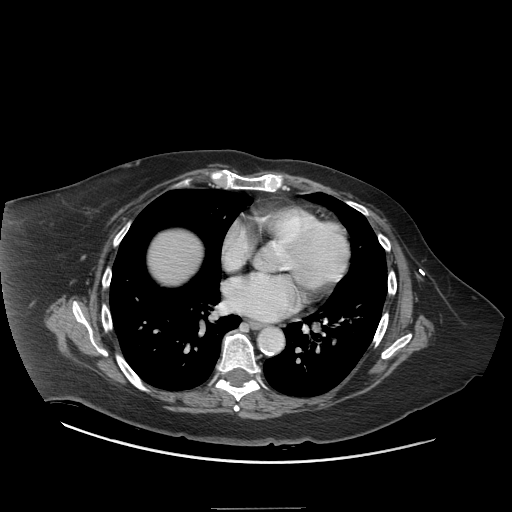
Contrast-enhanced abdominal CT (liver protocol), one axial slice; slice 76 of 81 in the series (ordered by position); reconstruction kernel STANDARD; soft-tissue window (W 400 / L 40 HU); 2.5 mm slice thickness; 512 × 512 image matrix, field of view 440 × 440 mm. From the clinical record (not read from this slice): diagnosis: hepatocellular carcinoma (patient treated with transarterial chemoembolisation; whether this scan precedes or follows treatment is not stated here); TNM stage (as recorded): Stage-II; Child-Pugh class: A; tumour differentiation: moderately differentiated; tumour nodularity: multinodular.
Outlined on this slice (semi-automatic segmentation, software-assisted and operator-edited):
- liver parenchyma outside the tumour (the mass and vessels are separate outlines, so this box may not span the whole liver): bounding box [x1, y1, x2, y2] px = [148, 230, 202, 284]